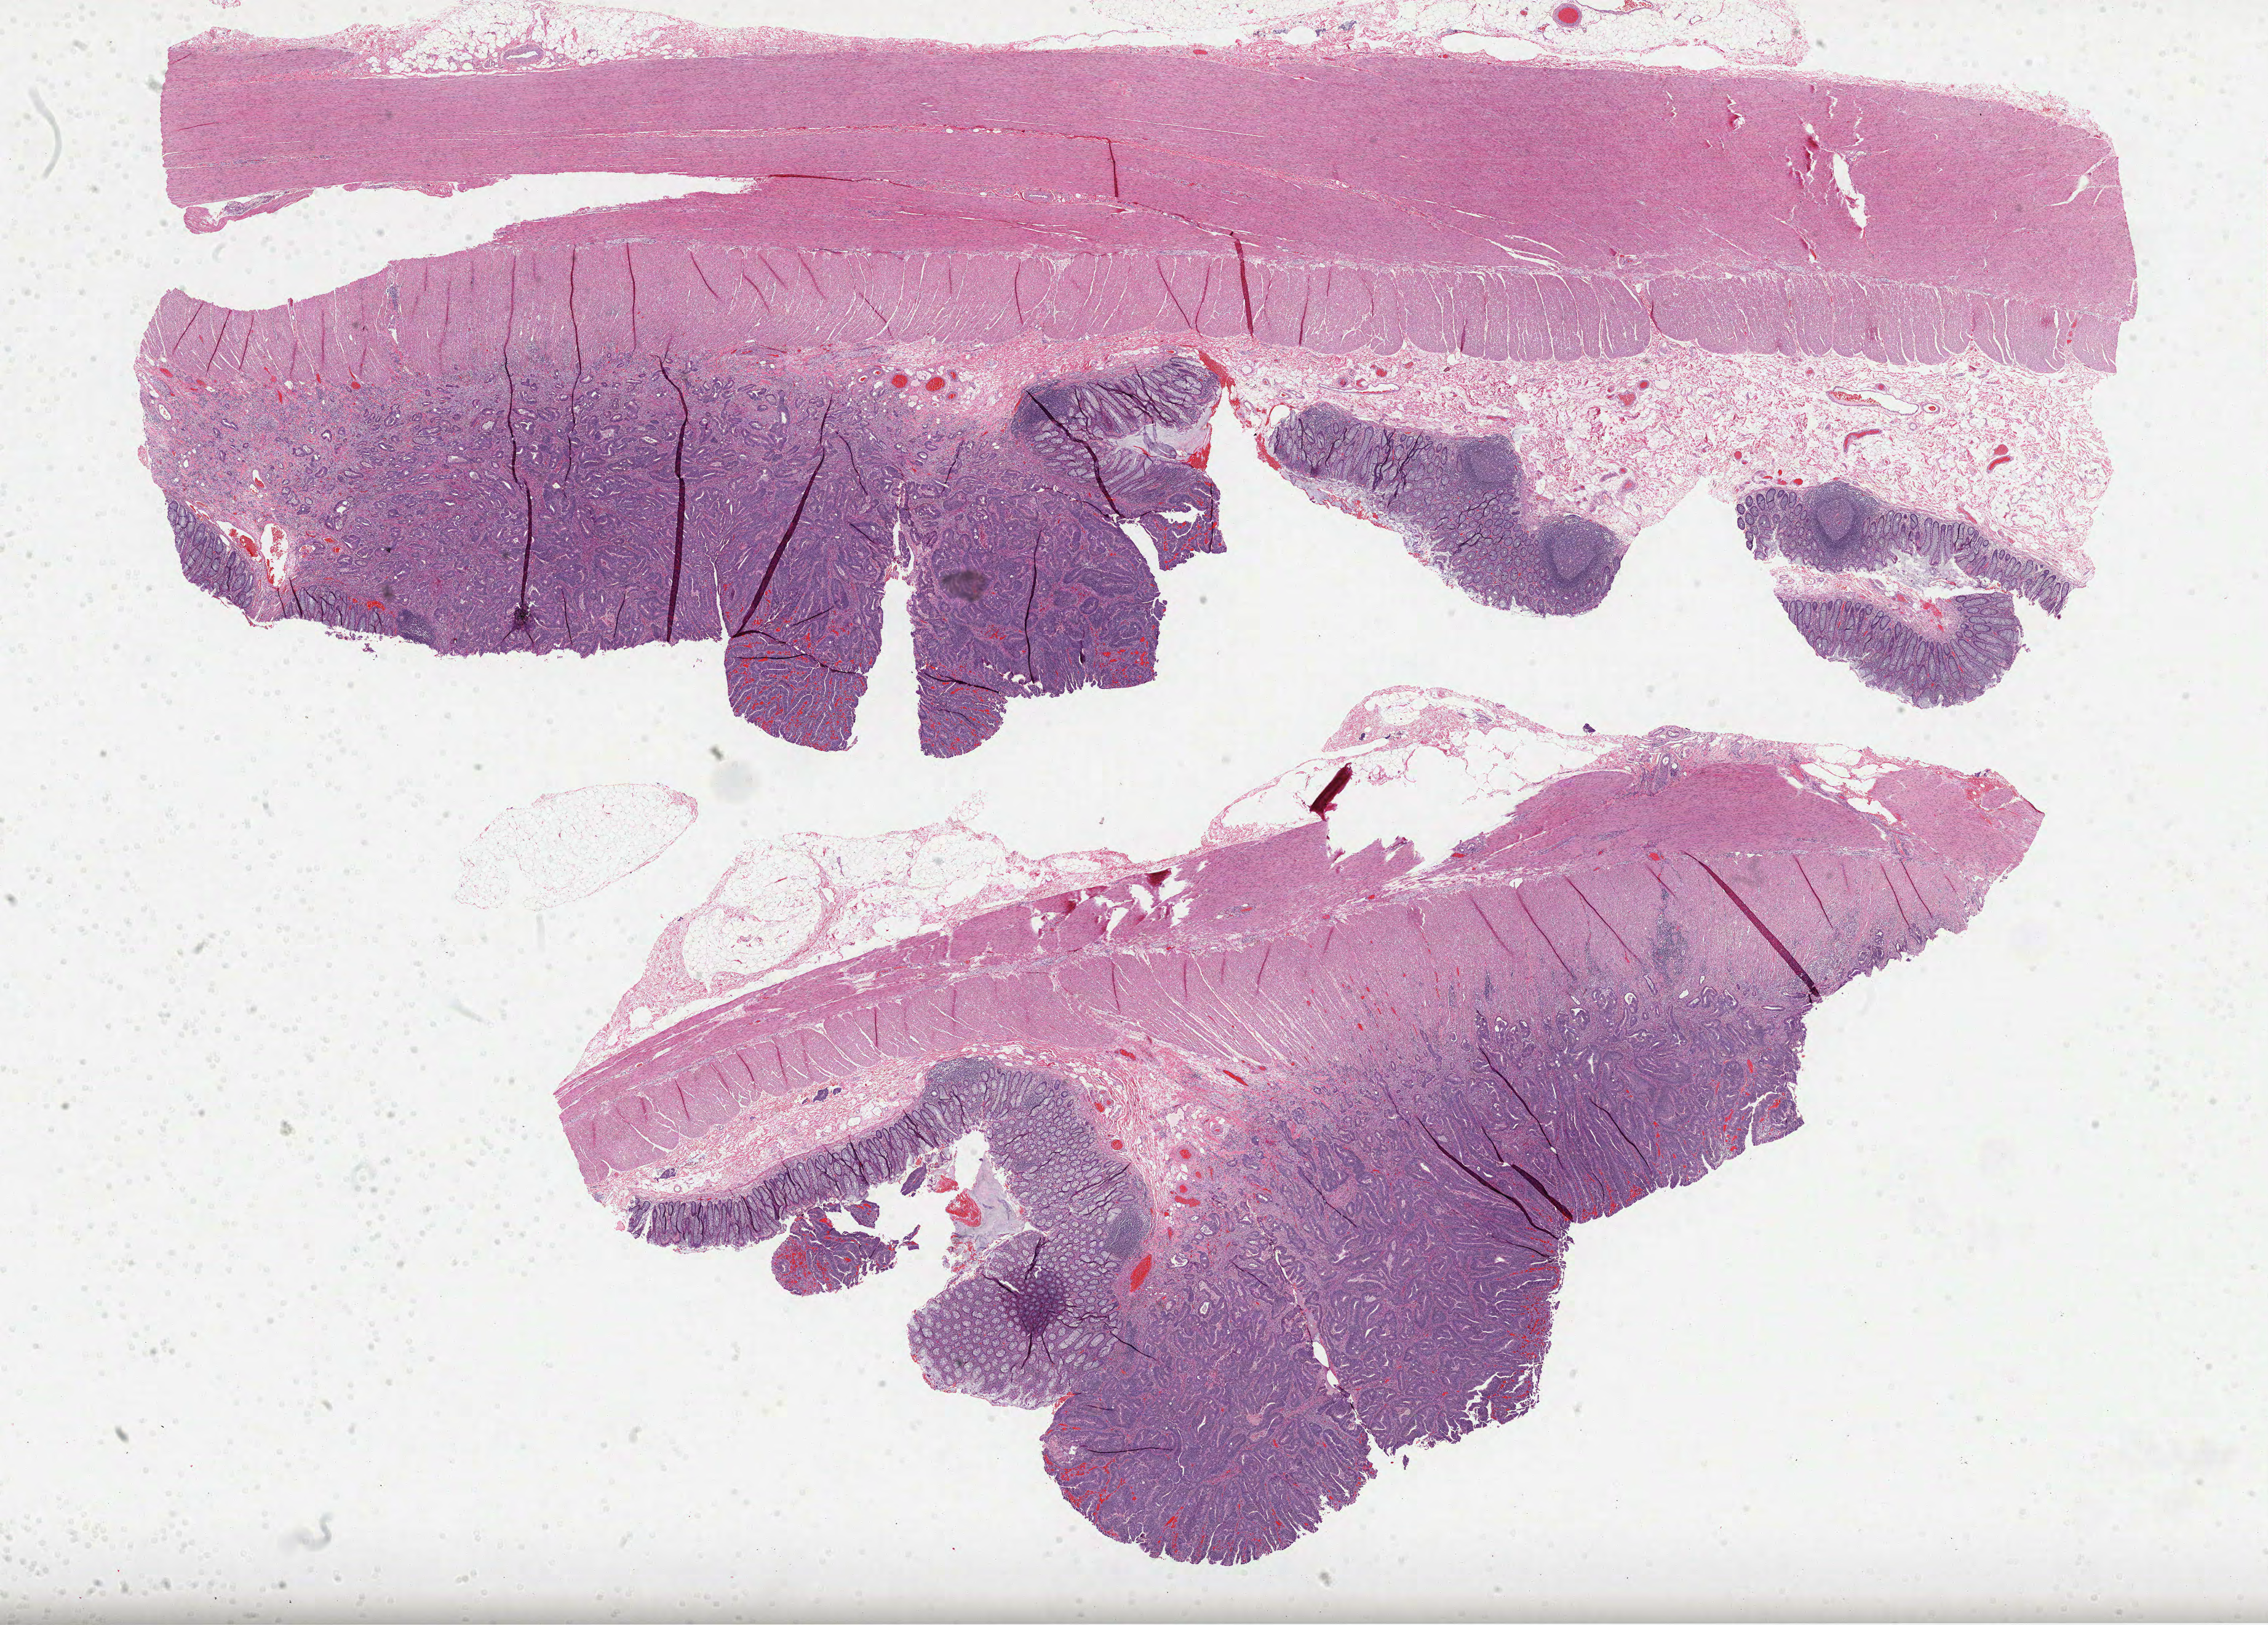
Whole-slide histology image, Hematoxylin and eosin (H&E) stained — whole scanned area (about 29.7 x 21.3 mm, from a 40x scan) shown as a low-resolution overview, FFPE section, sample: primary tumour, rectum. Male patient; age at initial diagnosis 68 years.
Histologic diagnosis: Adenocarcinoma, NOS. AJCC pathologic stage: I (6th edition).